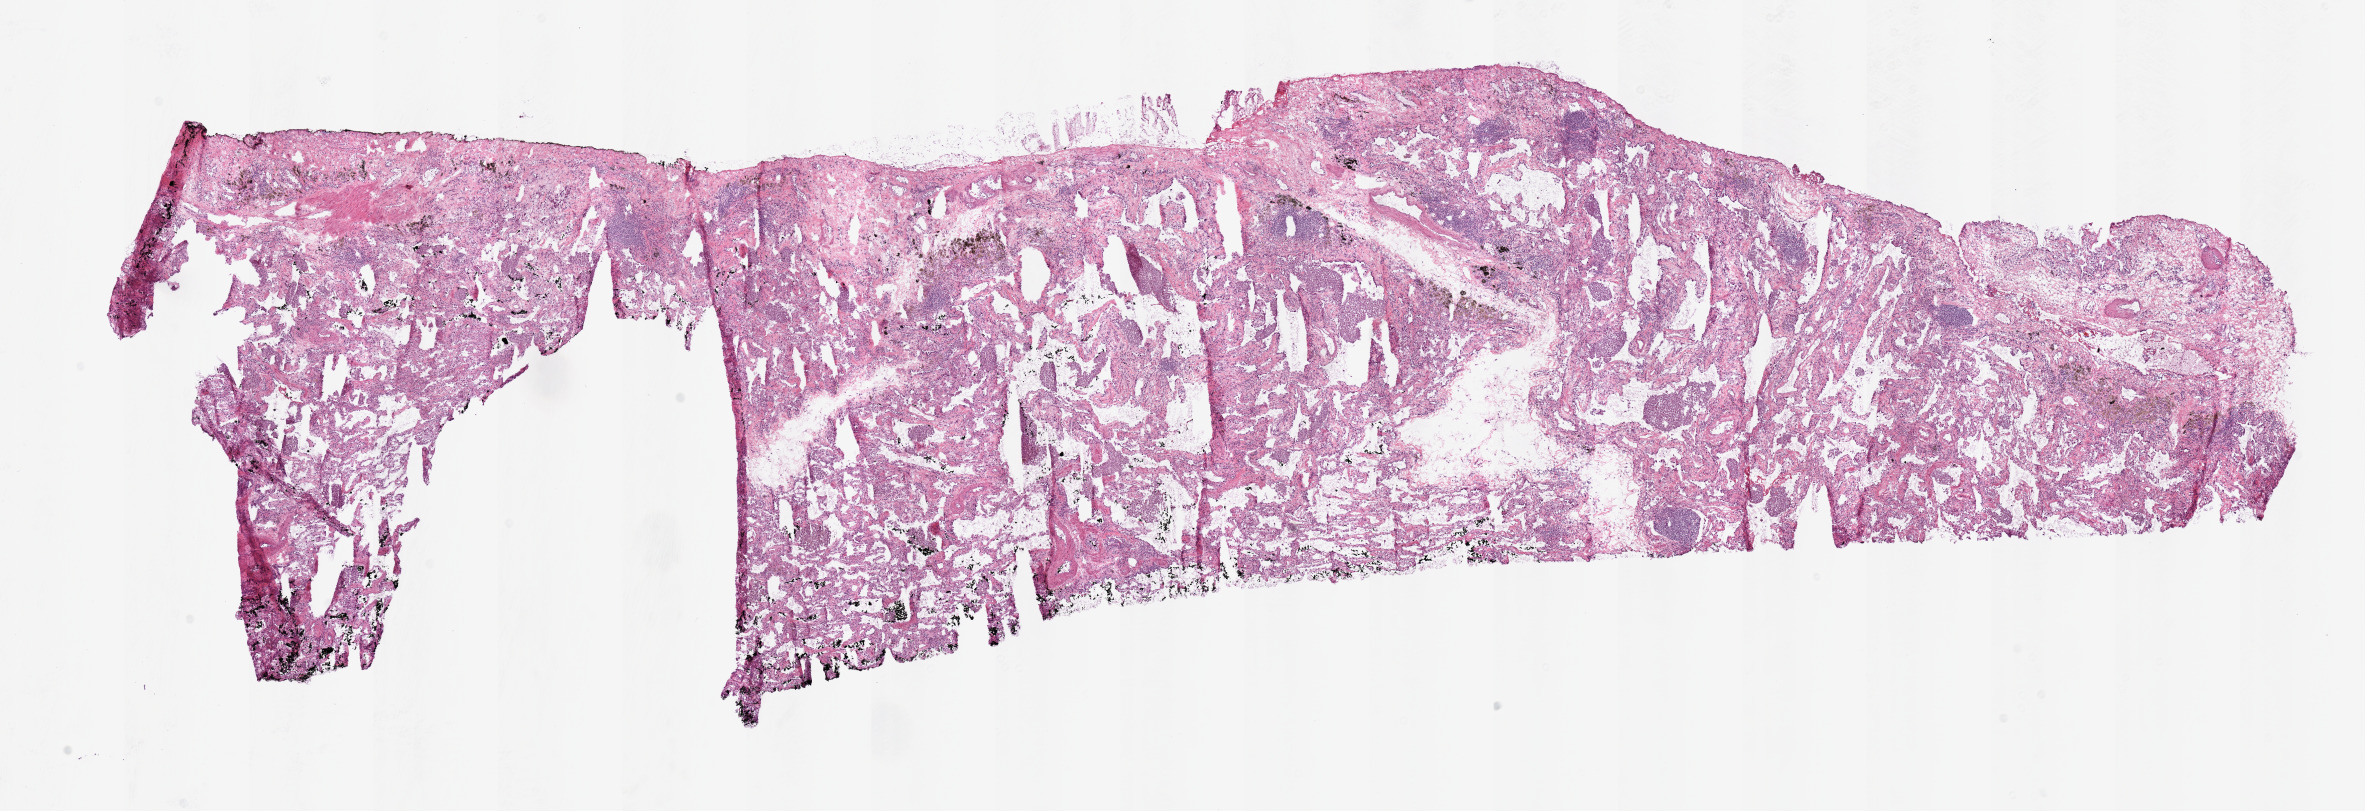
Digitized H&E tissue section (whole slide) — whole scanned area (about 18.7 x 6.4 mm, from a 20x scan) shown as a low-resolution overview; frozen section from the top of the tissue portion; lung, solid tissue normal (non-tumour tissue) sample. Male, age 52 years at initial diagnosis.
This section: solid tissue normal sample (biorepository sample class). Patient diagnosis: Adenocarcinoma, NOS (upper lobe, lung).